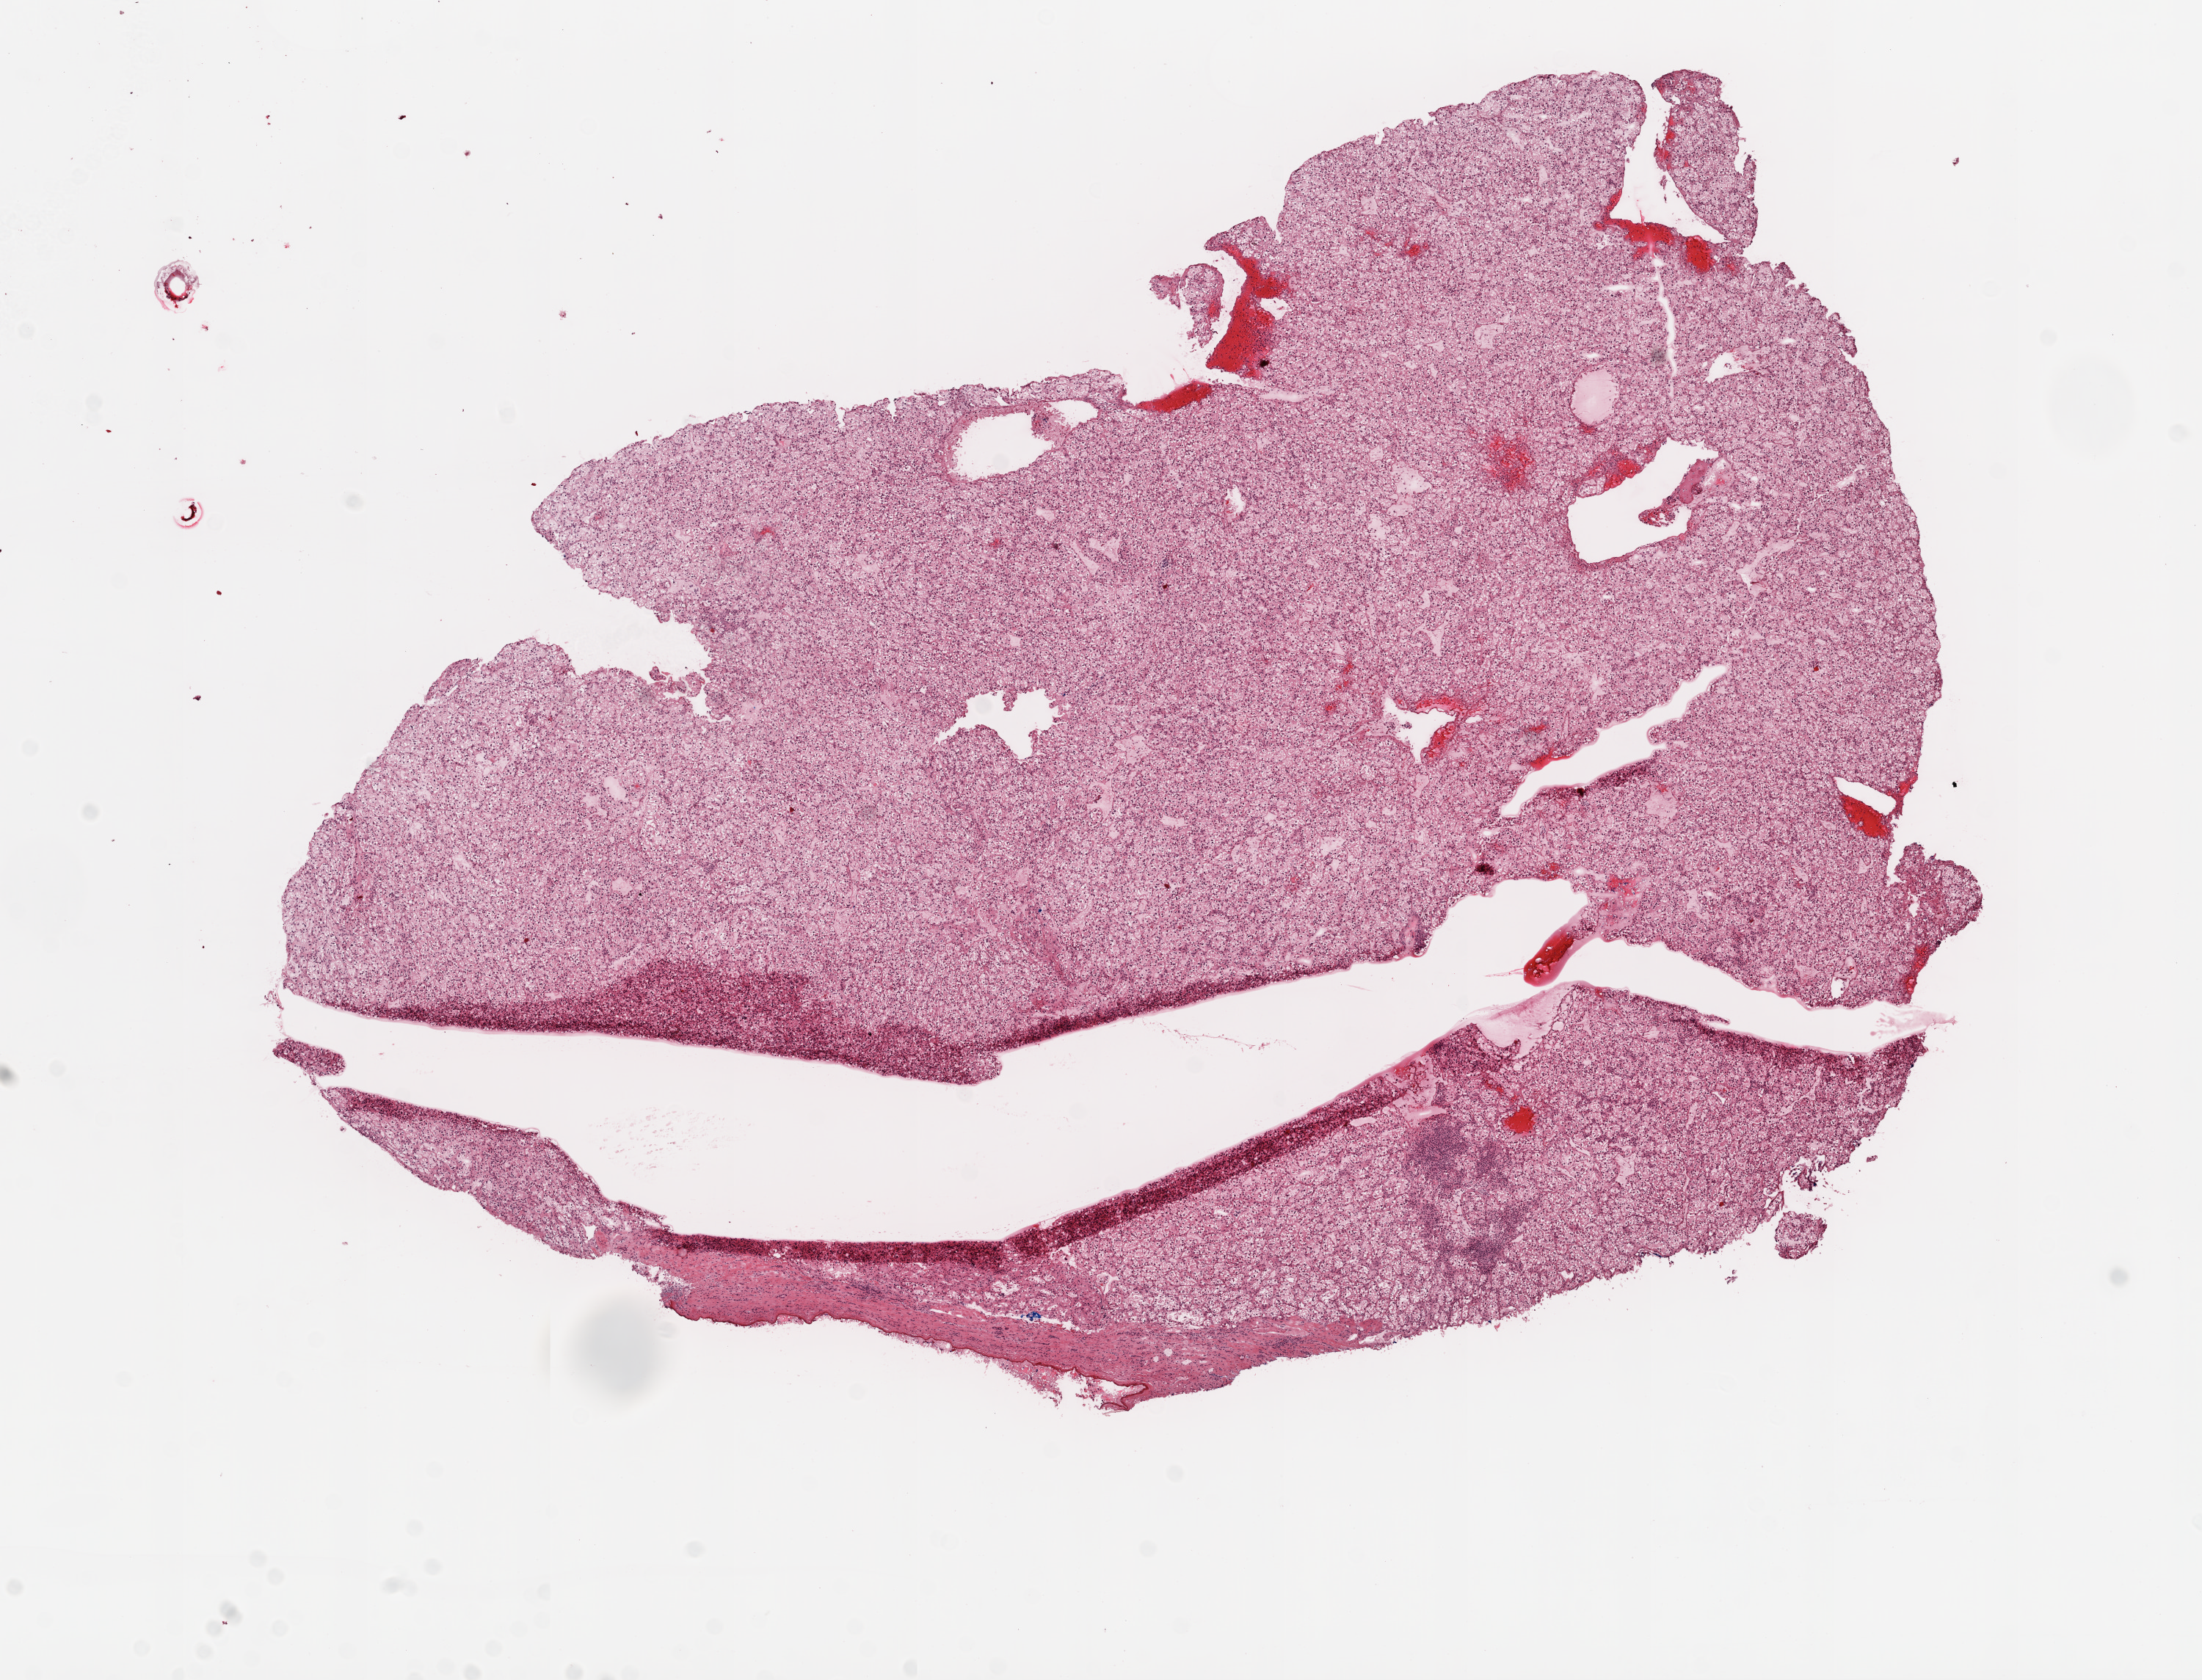
H&E-stained whole-slide image, a low-resolution overview of the entire scanned area, about 12.0 x 9.2 mm, frozen section, kidney, primary tumour sample. Female patient; age at initial diagnosis 55 years.
Diagnosis: Clear cell adenocarcinoma, NOS.